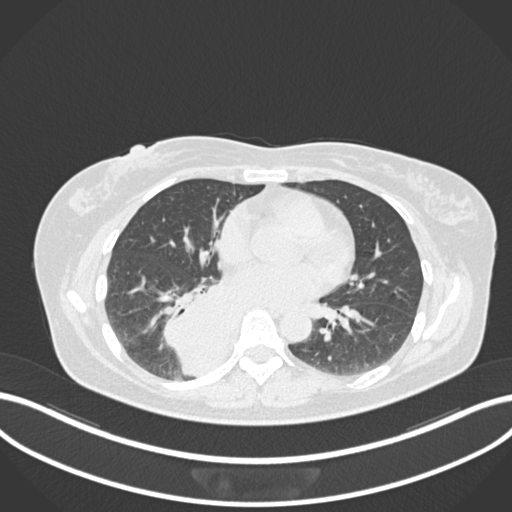
Chest CT, one axial slice; position 576 of 677 along the scan axis; lung window (W 1500 / L -600 HU); 1 mm slice thickness; 512 × 512 image matrix, field of view 400 × 400 mm. Female patient, age 54 years. From the clinical record (not read from this slice): clinical TNM (as recorded): T4 N0 M0.
Structures marked on this image (rectangle marked by the reading radiologist):
- lung tumour (recorded histology: adenocarcinoma): bounding box [x1, y1, x2, y2] px = [166, 276, 238, 375]